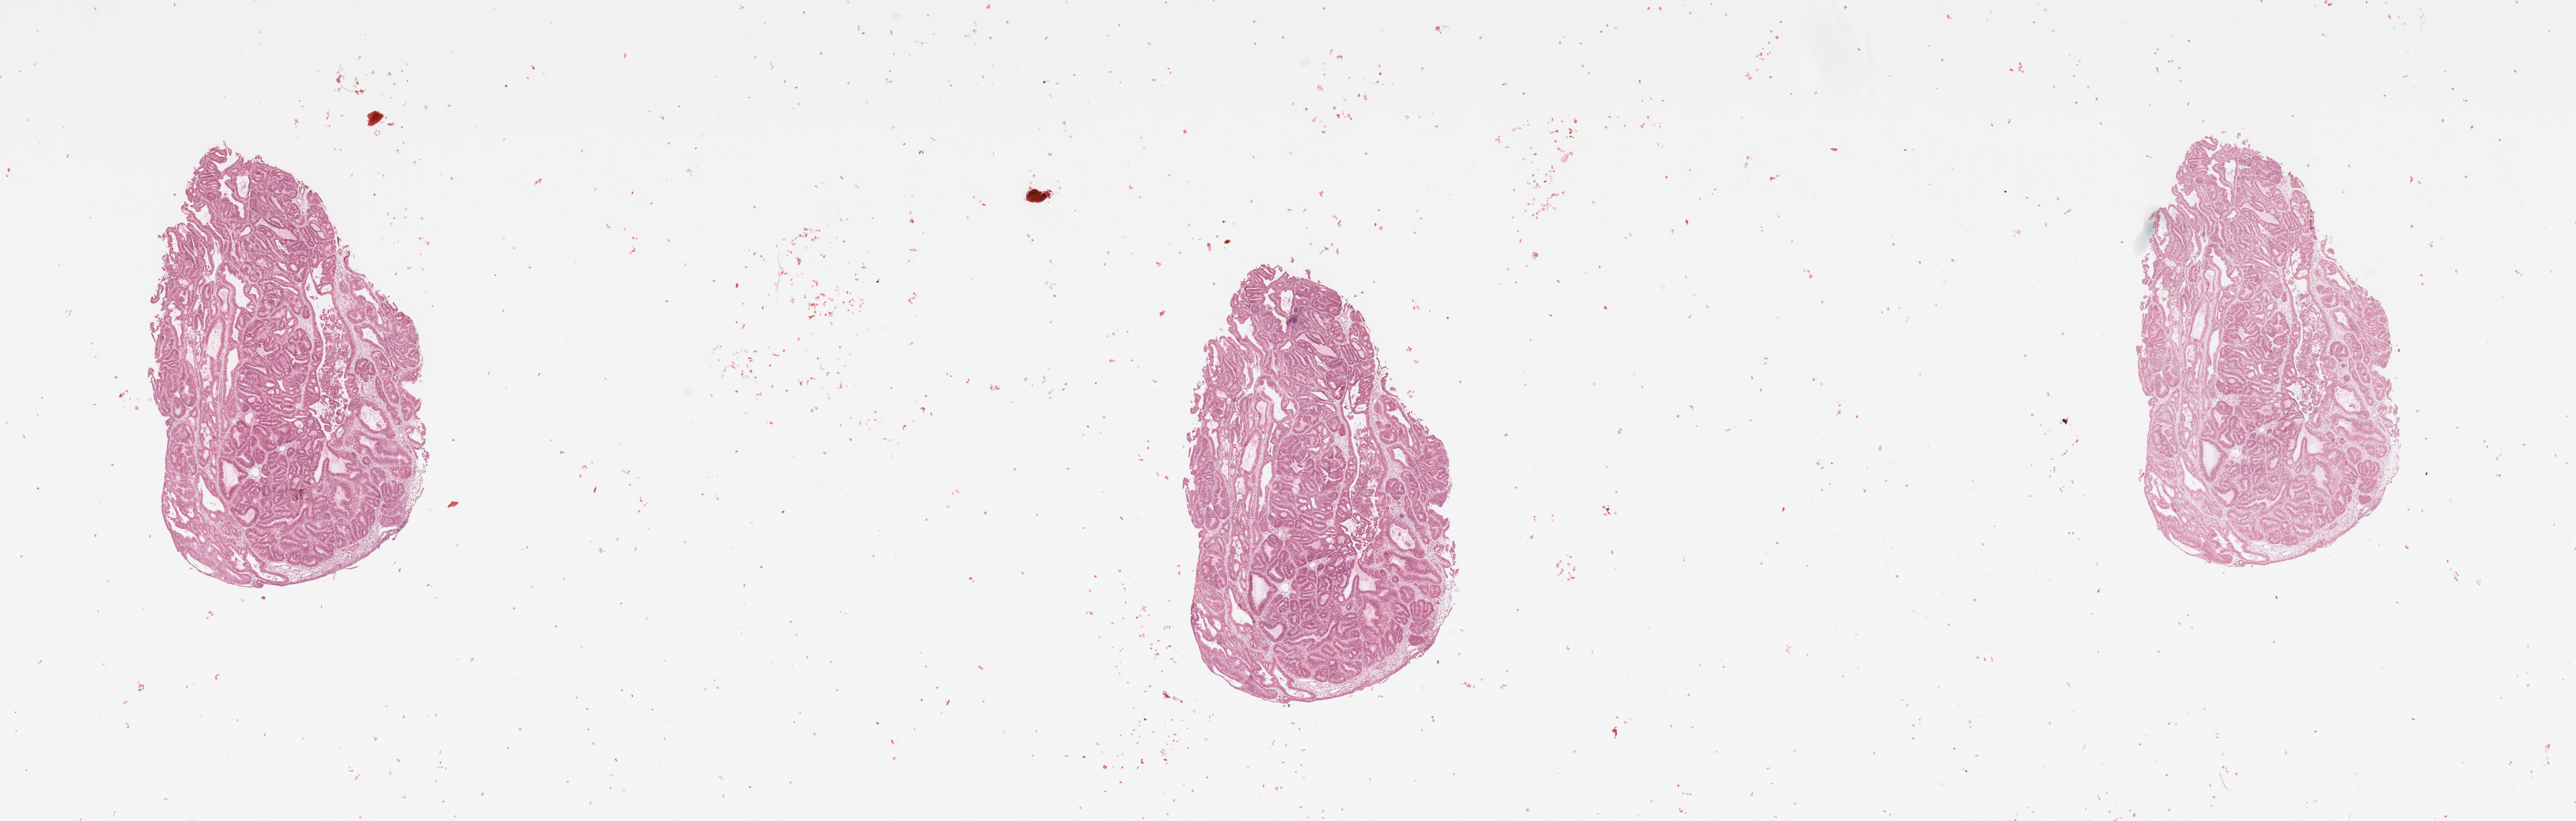
H&E whole-slide image — shown as a low-resolution overview of the whole scanned area (about 28.5 x 9.1 mm, acquisition: 20x scan). Tumour tissue sample, sampled site: uterus. Female, 68 y/o. Slide review estimates, as recorded: tumour nuclei 90%, necrosis 0%.
Histologic diagnosis: Endometrioid adenocarcinoma, NOS.